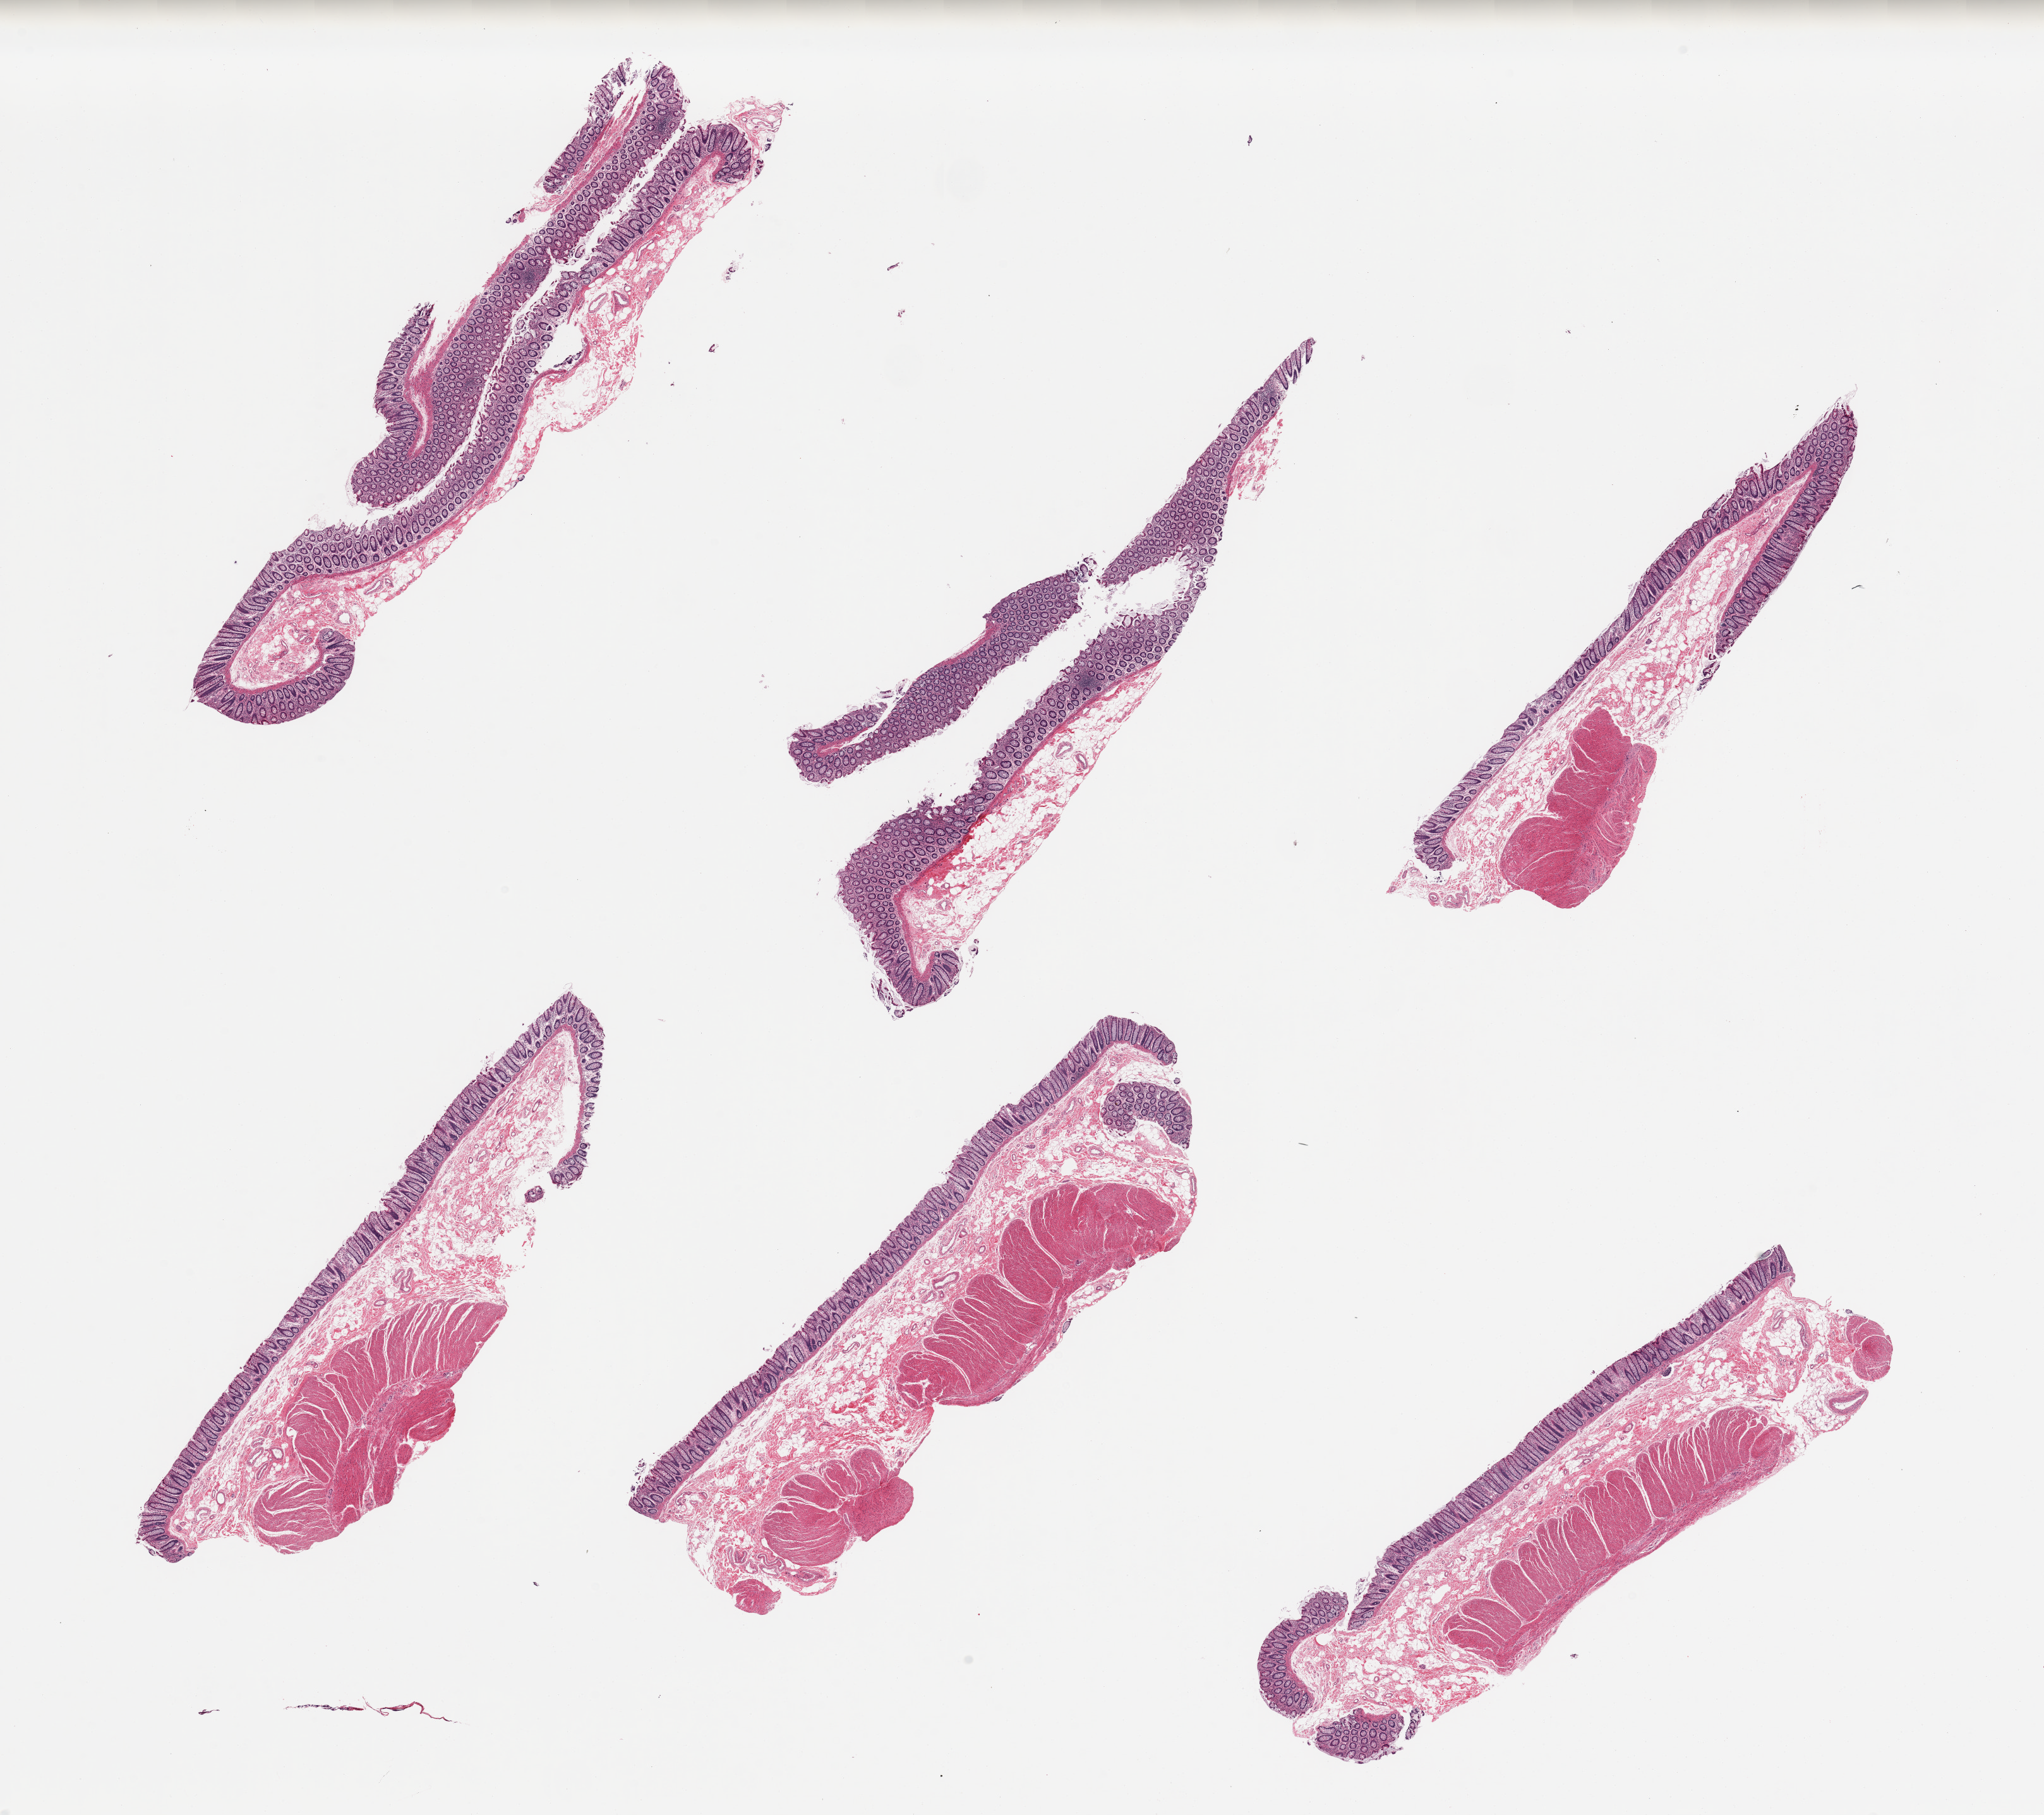
Whole-slide image, hematoxylin and eosin (H&E) stain, brightfield — whole scanned area (about 25.6 x 22.7 mm, slide scanned at 20x) shown as a low-resolution overview. PAXgene-fixed paraffin-embedded (PFPE) section. Sampled site (target tissue): transverse colon. Tissue donor sample. Donor: male.
* review note (as recorded): 6 pieces: 4 have full thickness (target); 2 have only mucosa